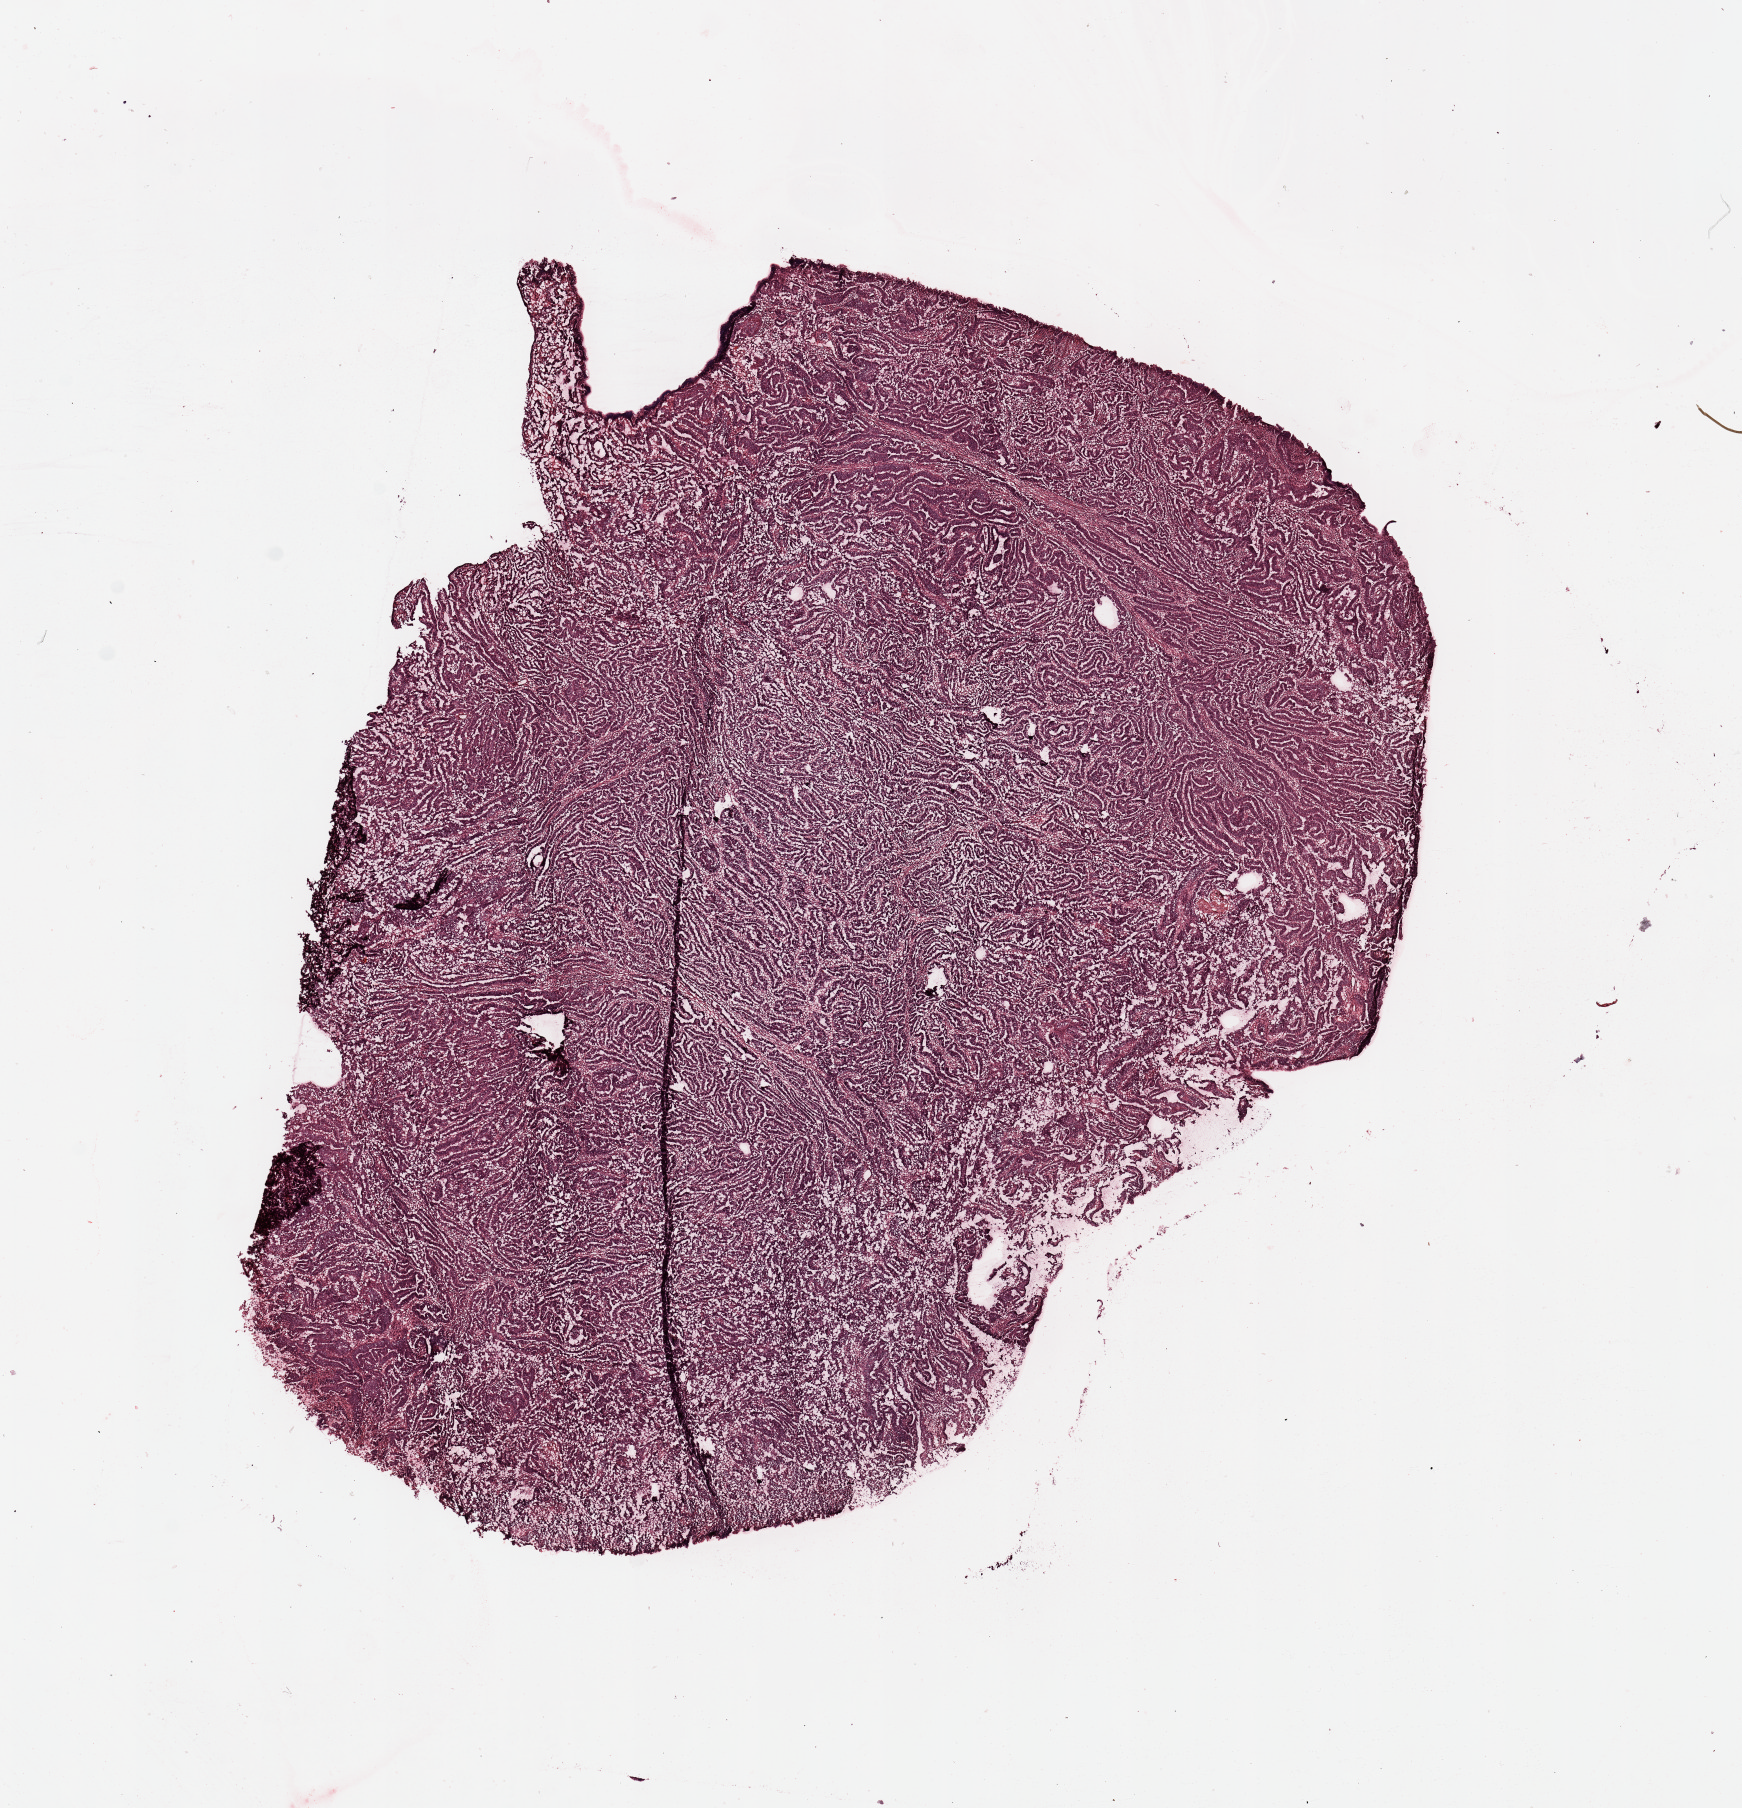
H&E whole-slide image — a low-resolution overview of the entire scanned area, about 13.8 x 14.3 mm (from a 20x scan), uterus, tumour tissue. Patient: female, age 64 years. Histologic grade: G1 (well differentiated).
AJCC pathologic stage: I. Histologic diagnosis: Endometrioid adenocarcinoma, NOS.